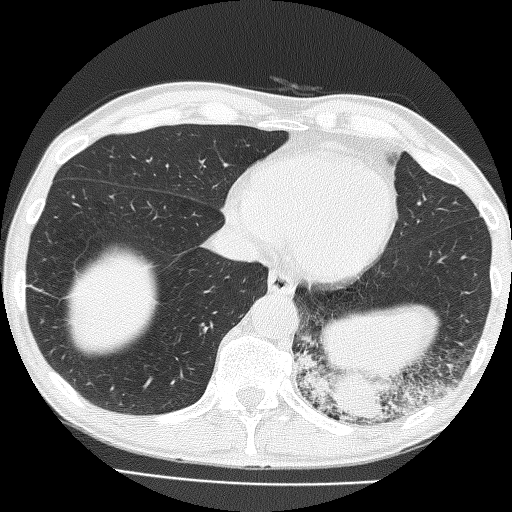
Low-dose screening chest CT, one axial slice. Position 49 of 160 along the scan axis. Reconstruction kernel FC51. Lung window (W 1500 / L -600 HU). 2 mm slice thickness. 512 × 512 image matrix, field of view 324 × 324 mm.
Annotated regions visible in this slice (outlined manually by an expert reader):
- lesion 1 (tumor, lower lobe of left lung): box from (x=325, y=370) to (x=387, y=424) px